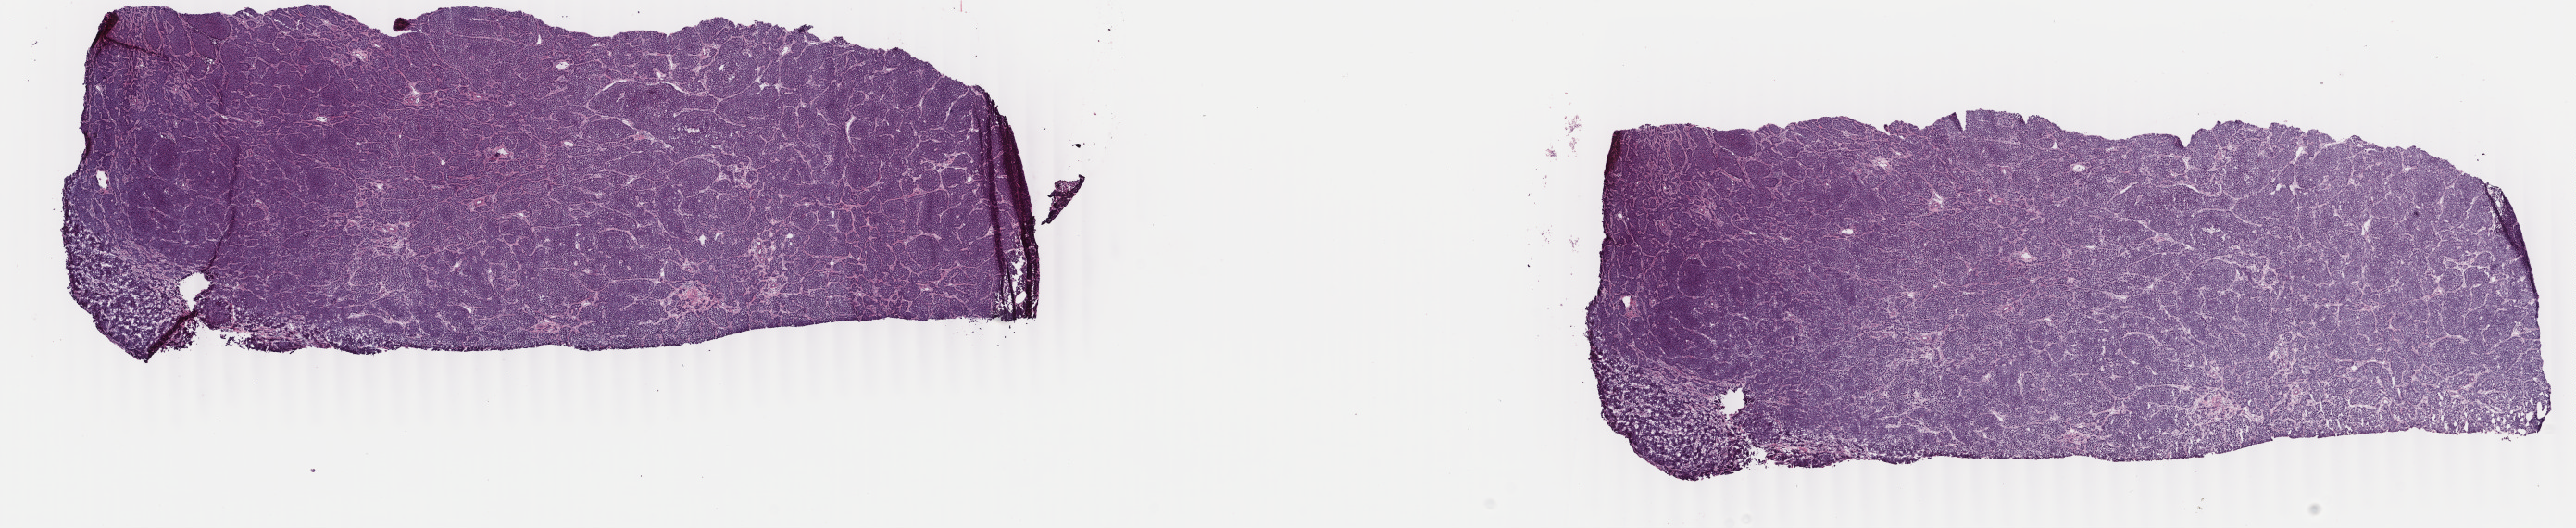
Whole-slide histology image, H&E-stained, low-resolution overview of the scanned area, about 22.1 x 4.5 mm; frozen section from the bottom of the tissue portion; sample: primary tumour, breast. Female patient; age at initial diagnosis 68 years. Pathologist review of this section (percent, as recorded): tumour cells 90%, tumour nuclei 80%, normal cells 0%, stromal cells 10%, necrosis 0%. Infiltration values recorded for this section: lymphocyte infiltration 0%, monocyte infiltration 0%, neutrophil infiltration 0%.
Diagnosis: Infiltrating duct carcinoma, NOS. AJCC pathologic stage: IIB. Lymph nodes positive (case pathology): 1 of 27 examined.